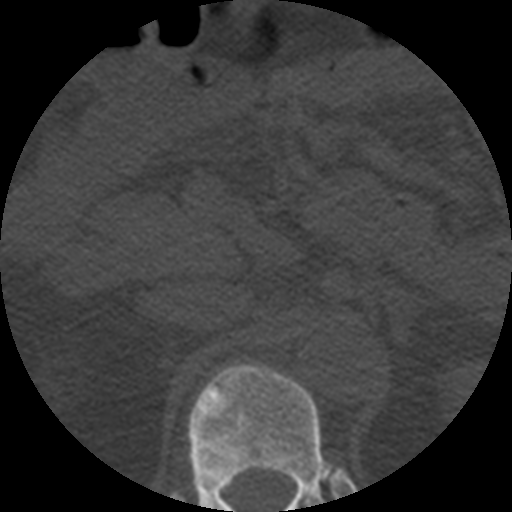
CT including the spine, one axial slice; slice 212 of 508 in the series (ordered by position); reconstruction kernel STANDARD; 120 kVp; bone window (W 1800 / L 400 HU); 1.25 mm slice thickness; 512 × 512 image matrix, field of view 160 × 160 mm. Patient age 57 years. Case-level facts recorded for this patient, not image findings: primary cancer: prostate.
Outlined on this slice (semi-automatically segmented with operator editing):
- T12 vertebra: bounding box (x1, y1, x2, y2) in pixels: (178, 364, 348, 512)